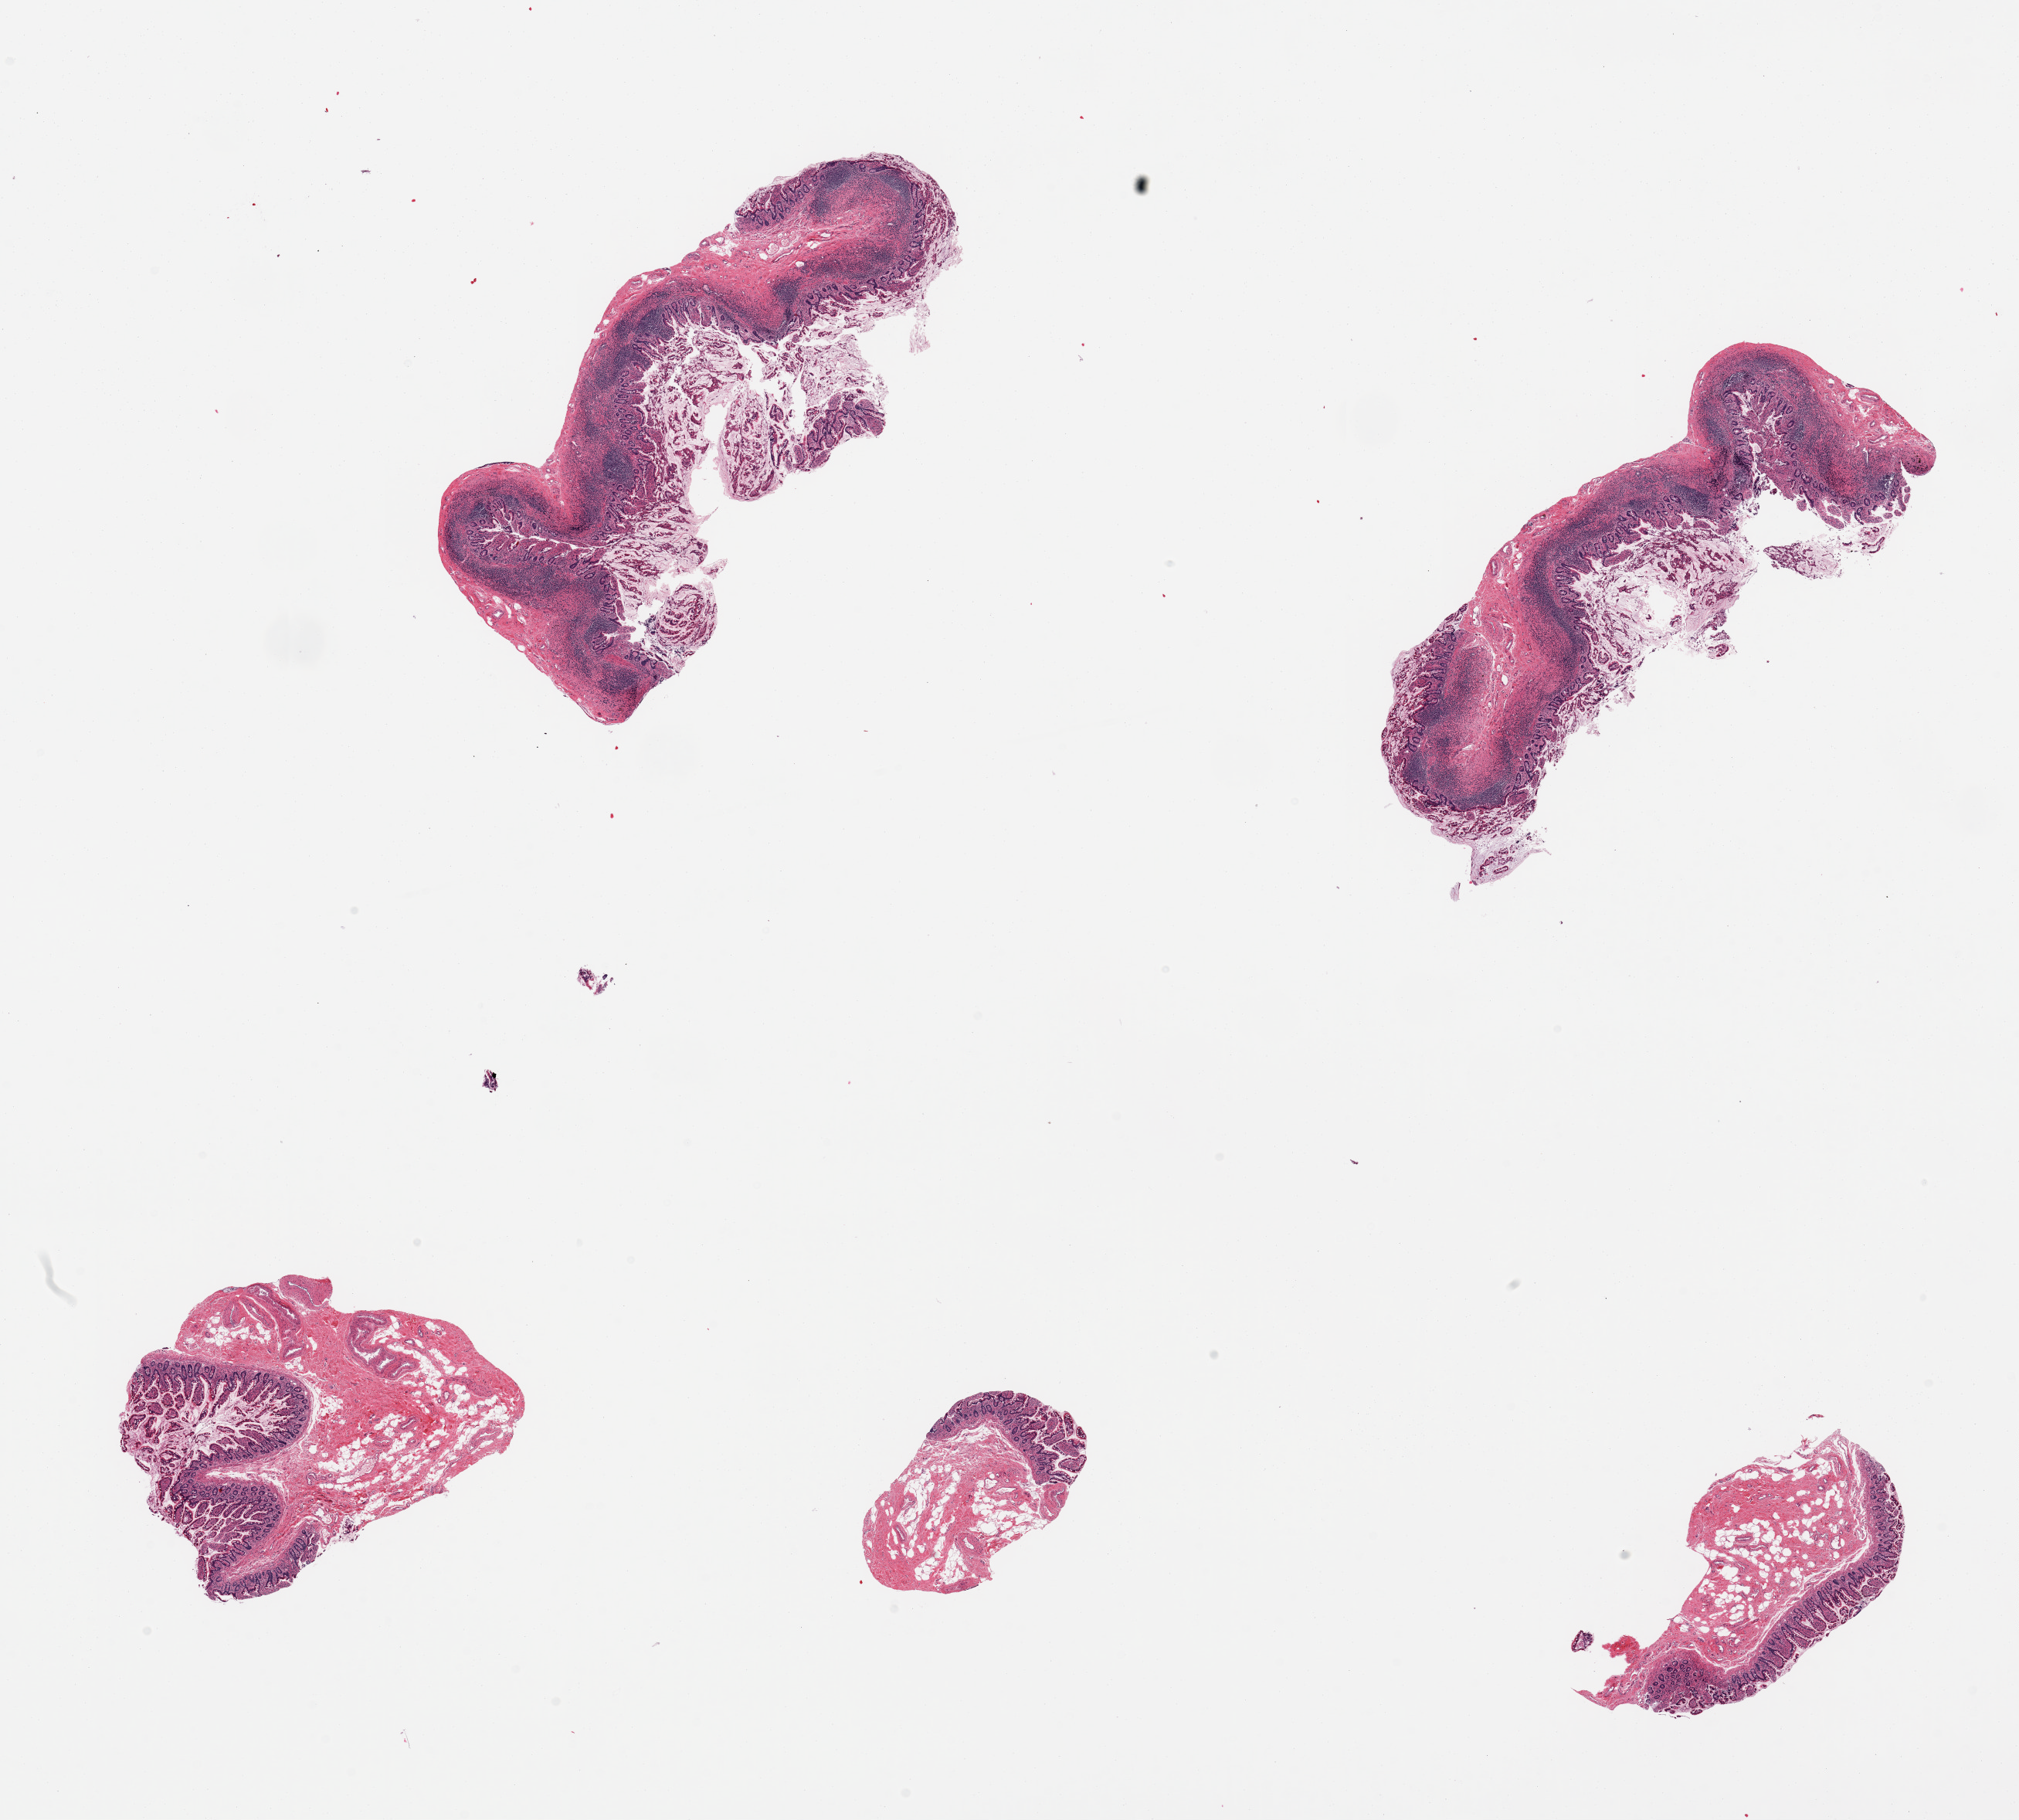
H&E whole-slide image — whole scanned area (about 20.7 x 18.6 mm, acquisition: 20x scan) shown as a low-resolution overview, PAXgene-fixed, paraffin-embedded tissue, target tissue: ileum, tissue donor sample.
- pathologist's review note for this sample: 5 pieces; mucosa with good lymphoid component in 2 of 5 pieces